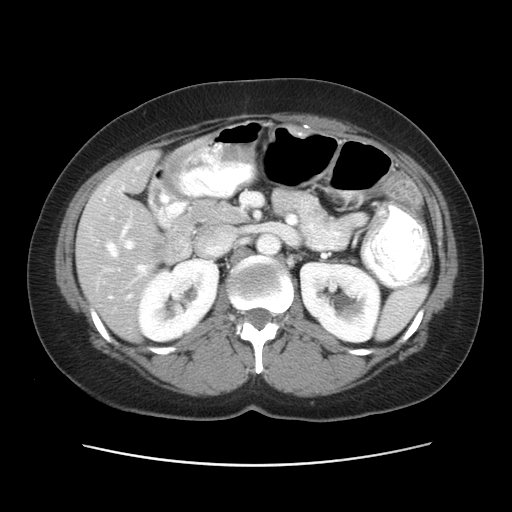
Contrast-enhanced abdominal CT, one axial slice. Position 27 of 52 along the scan axis. Reconstruction kernel STANDARD. 120 kVp. Intravenous contrast given. Soft-tissue window (W 400 / L 40 HU). 5 mm slice thickness. 512 × 512 image matrix, field of view 362 × 362 mm. Female patient, age 48 years. From the clinical record (not read from this slice): diagnosis: colorectal cancer liver metastases, imaged before liver resection; multiple liver metastases: yes; largest metastasis: 4.5 cm.
Structures marked on this image (expert manual segmentation):
- hepatic veins: bounding box (x1, y1, x2, y2) in pixels: (107, 188, 147, 298)
- liver: (78, 154, 156, 339)
- portal vein (with intrahepatic branches): (124, 168, 138, 249)